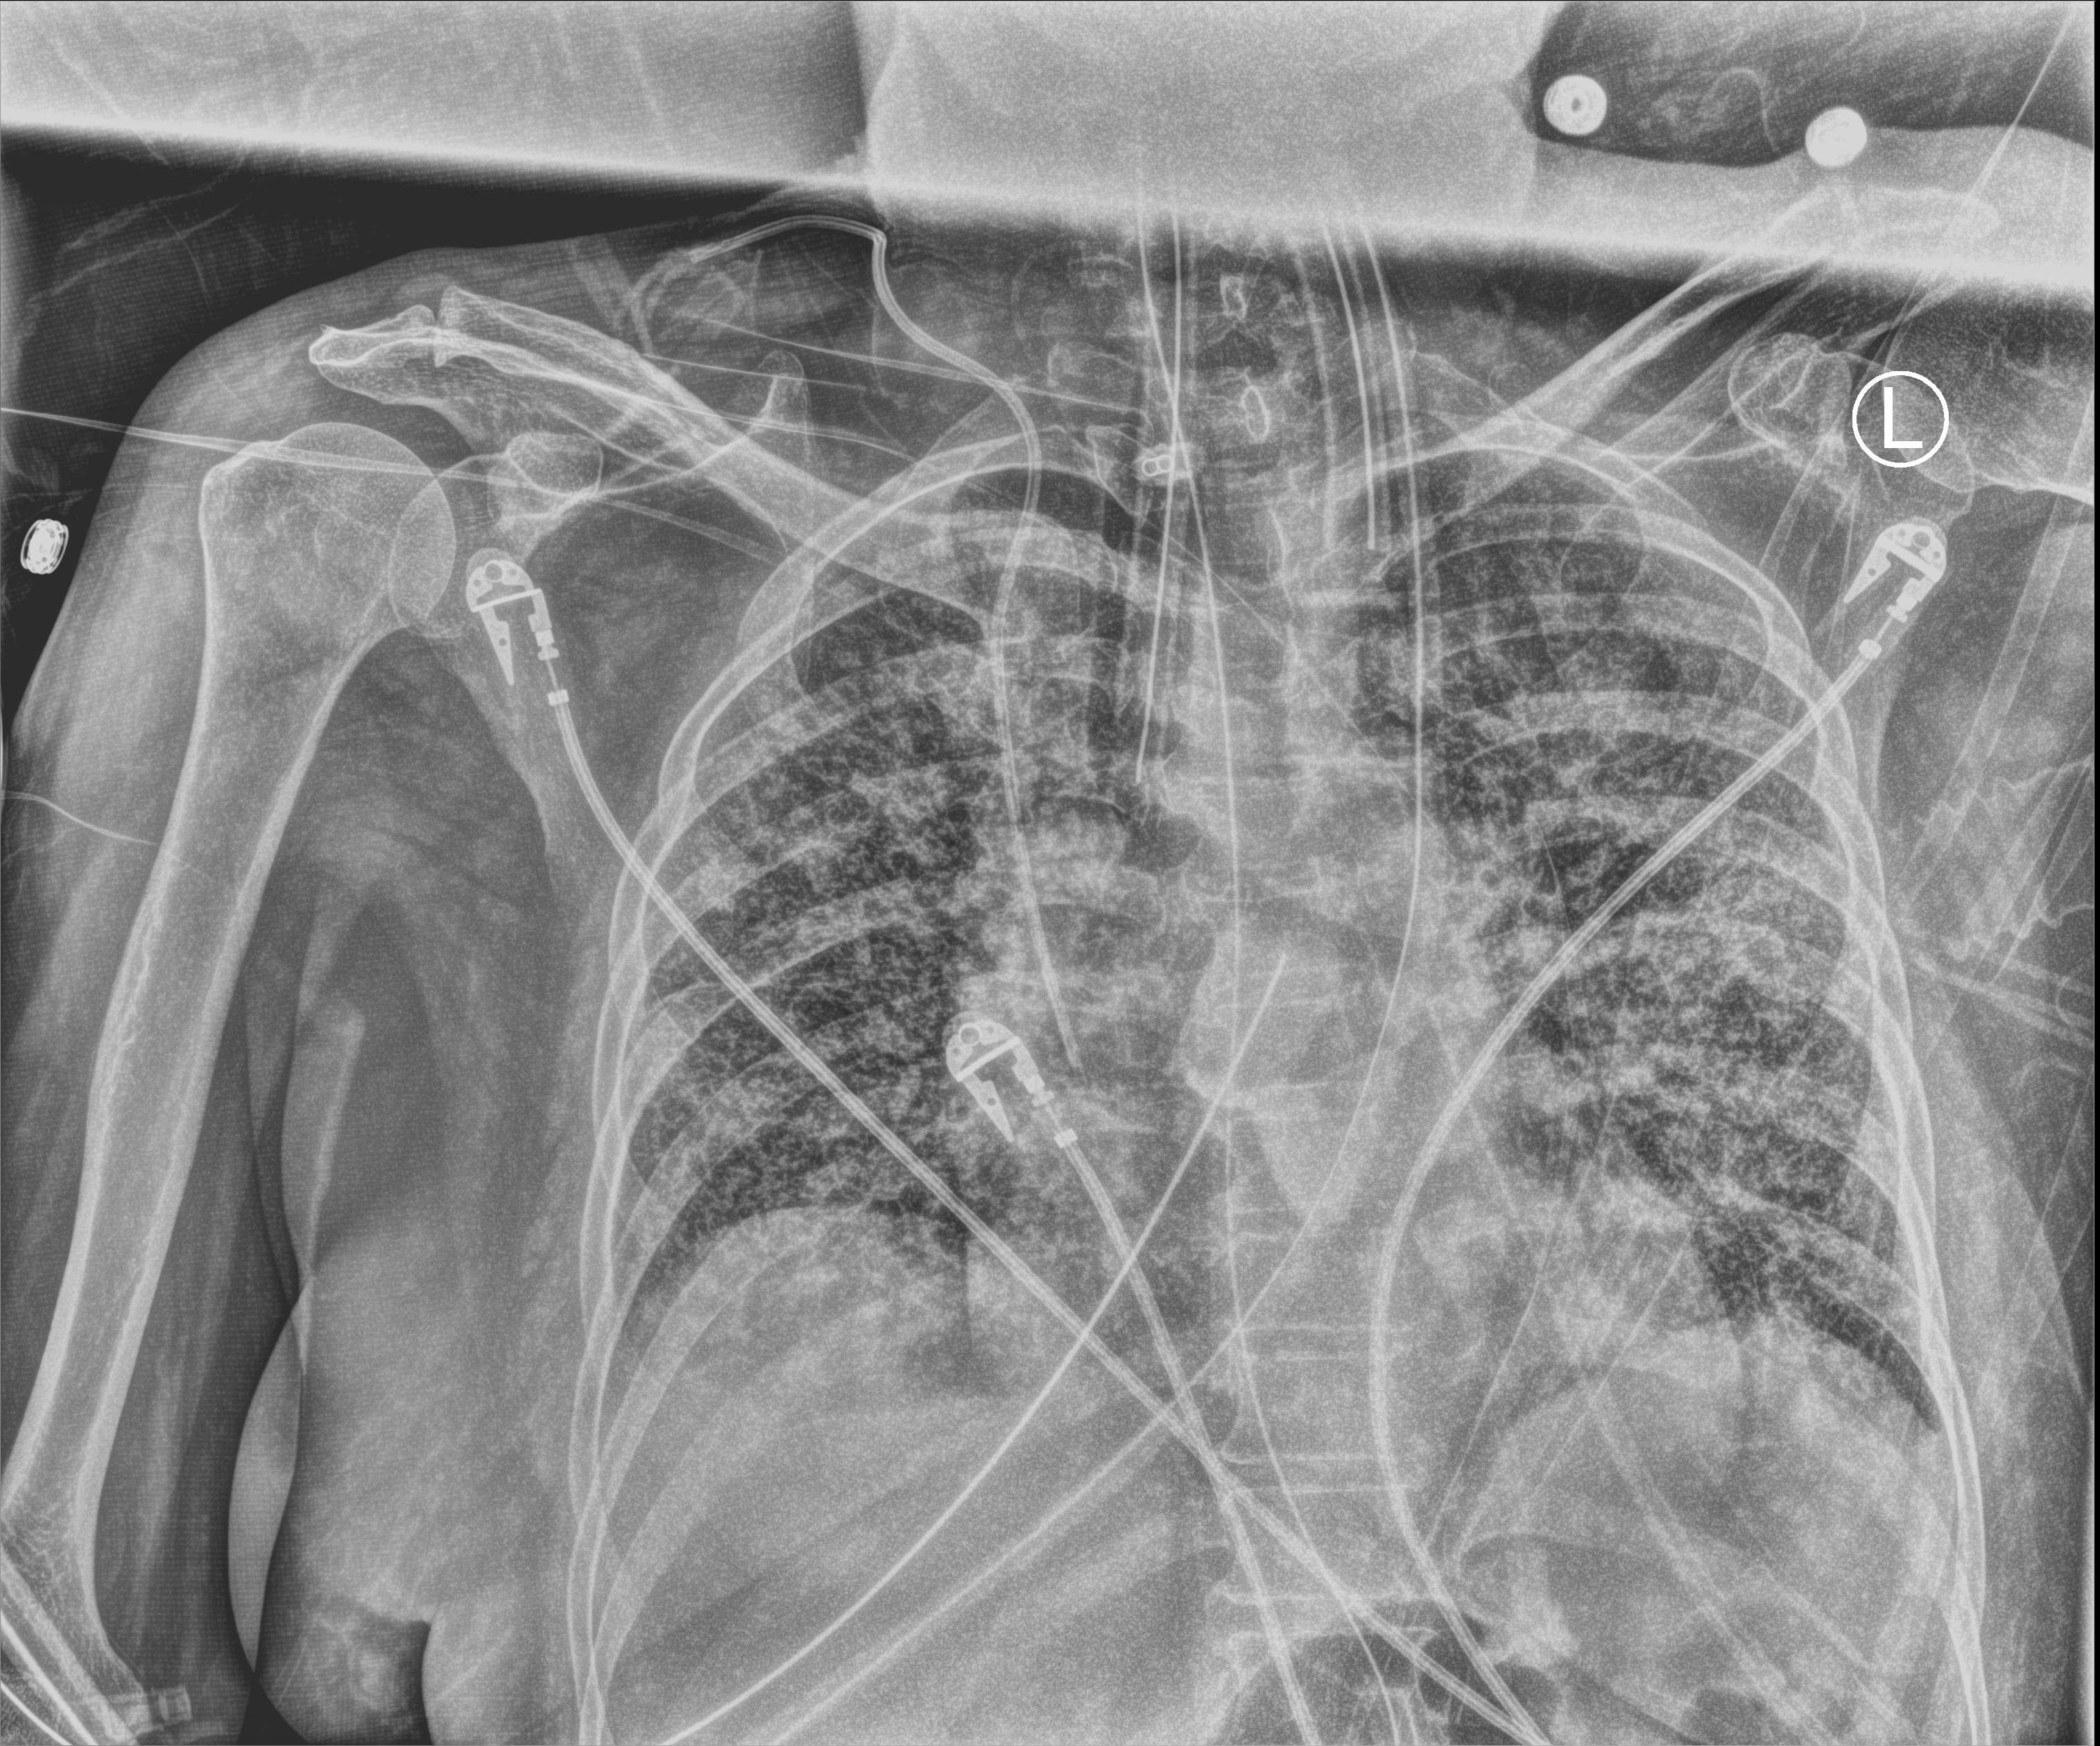
Portable chest radiograph; anteroposterior (AP) projection. Female patient hospitalised with COVID-19, age 60–74 years.
Hospital-stay facts (about this admission, not read from this image; timing relative to this image not recorded): other chronic lung disease (admission record): yes; hypertension (admission record): no; mechanically ventilated during this hospital stay: yes.